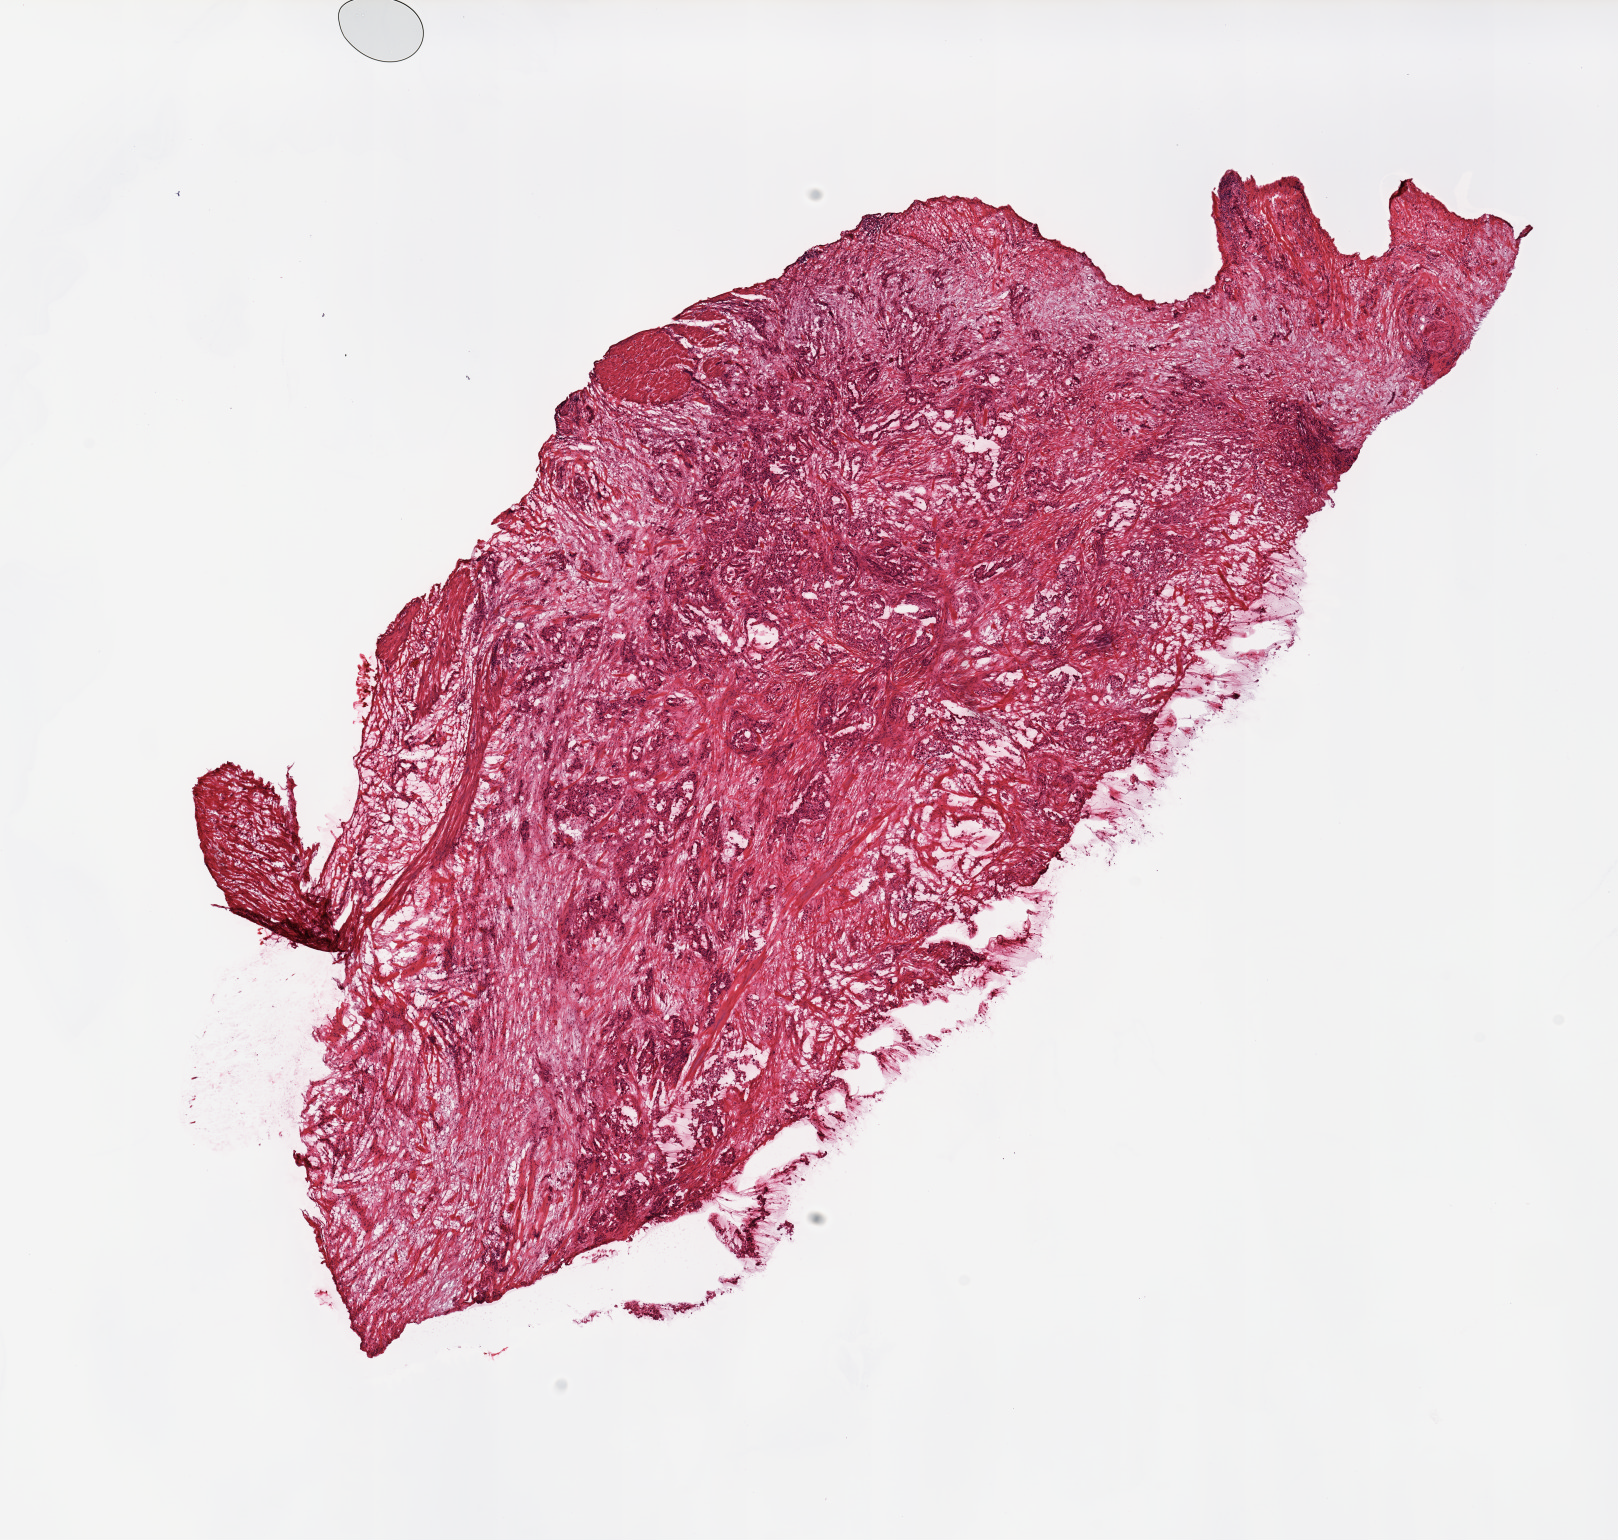
Digitized Hematoxylin and eosin (H&E) stained tissue section (whole slide) — a low-resolution overview of the entire scanned area, about 12.8 x 12.2 mm (from a 20x scan), tumour tissue sample, sampled site: pancreas. 61-year-old female patient. Histologic grade: G2 (moderately differentiated). Slide review estimates, as recorded: tumour nuclei 50%, necrosis 0%.
* diagnosis: Infiltrating duct carcinoma, NOS
* primary tumour site (as recorded): head
* AJCC pathologic stage: IIB